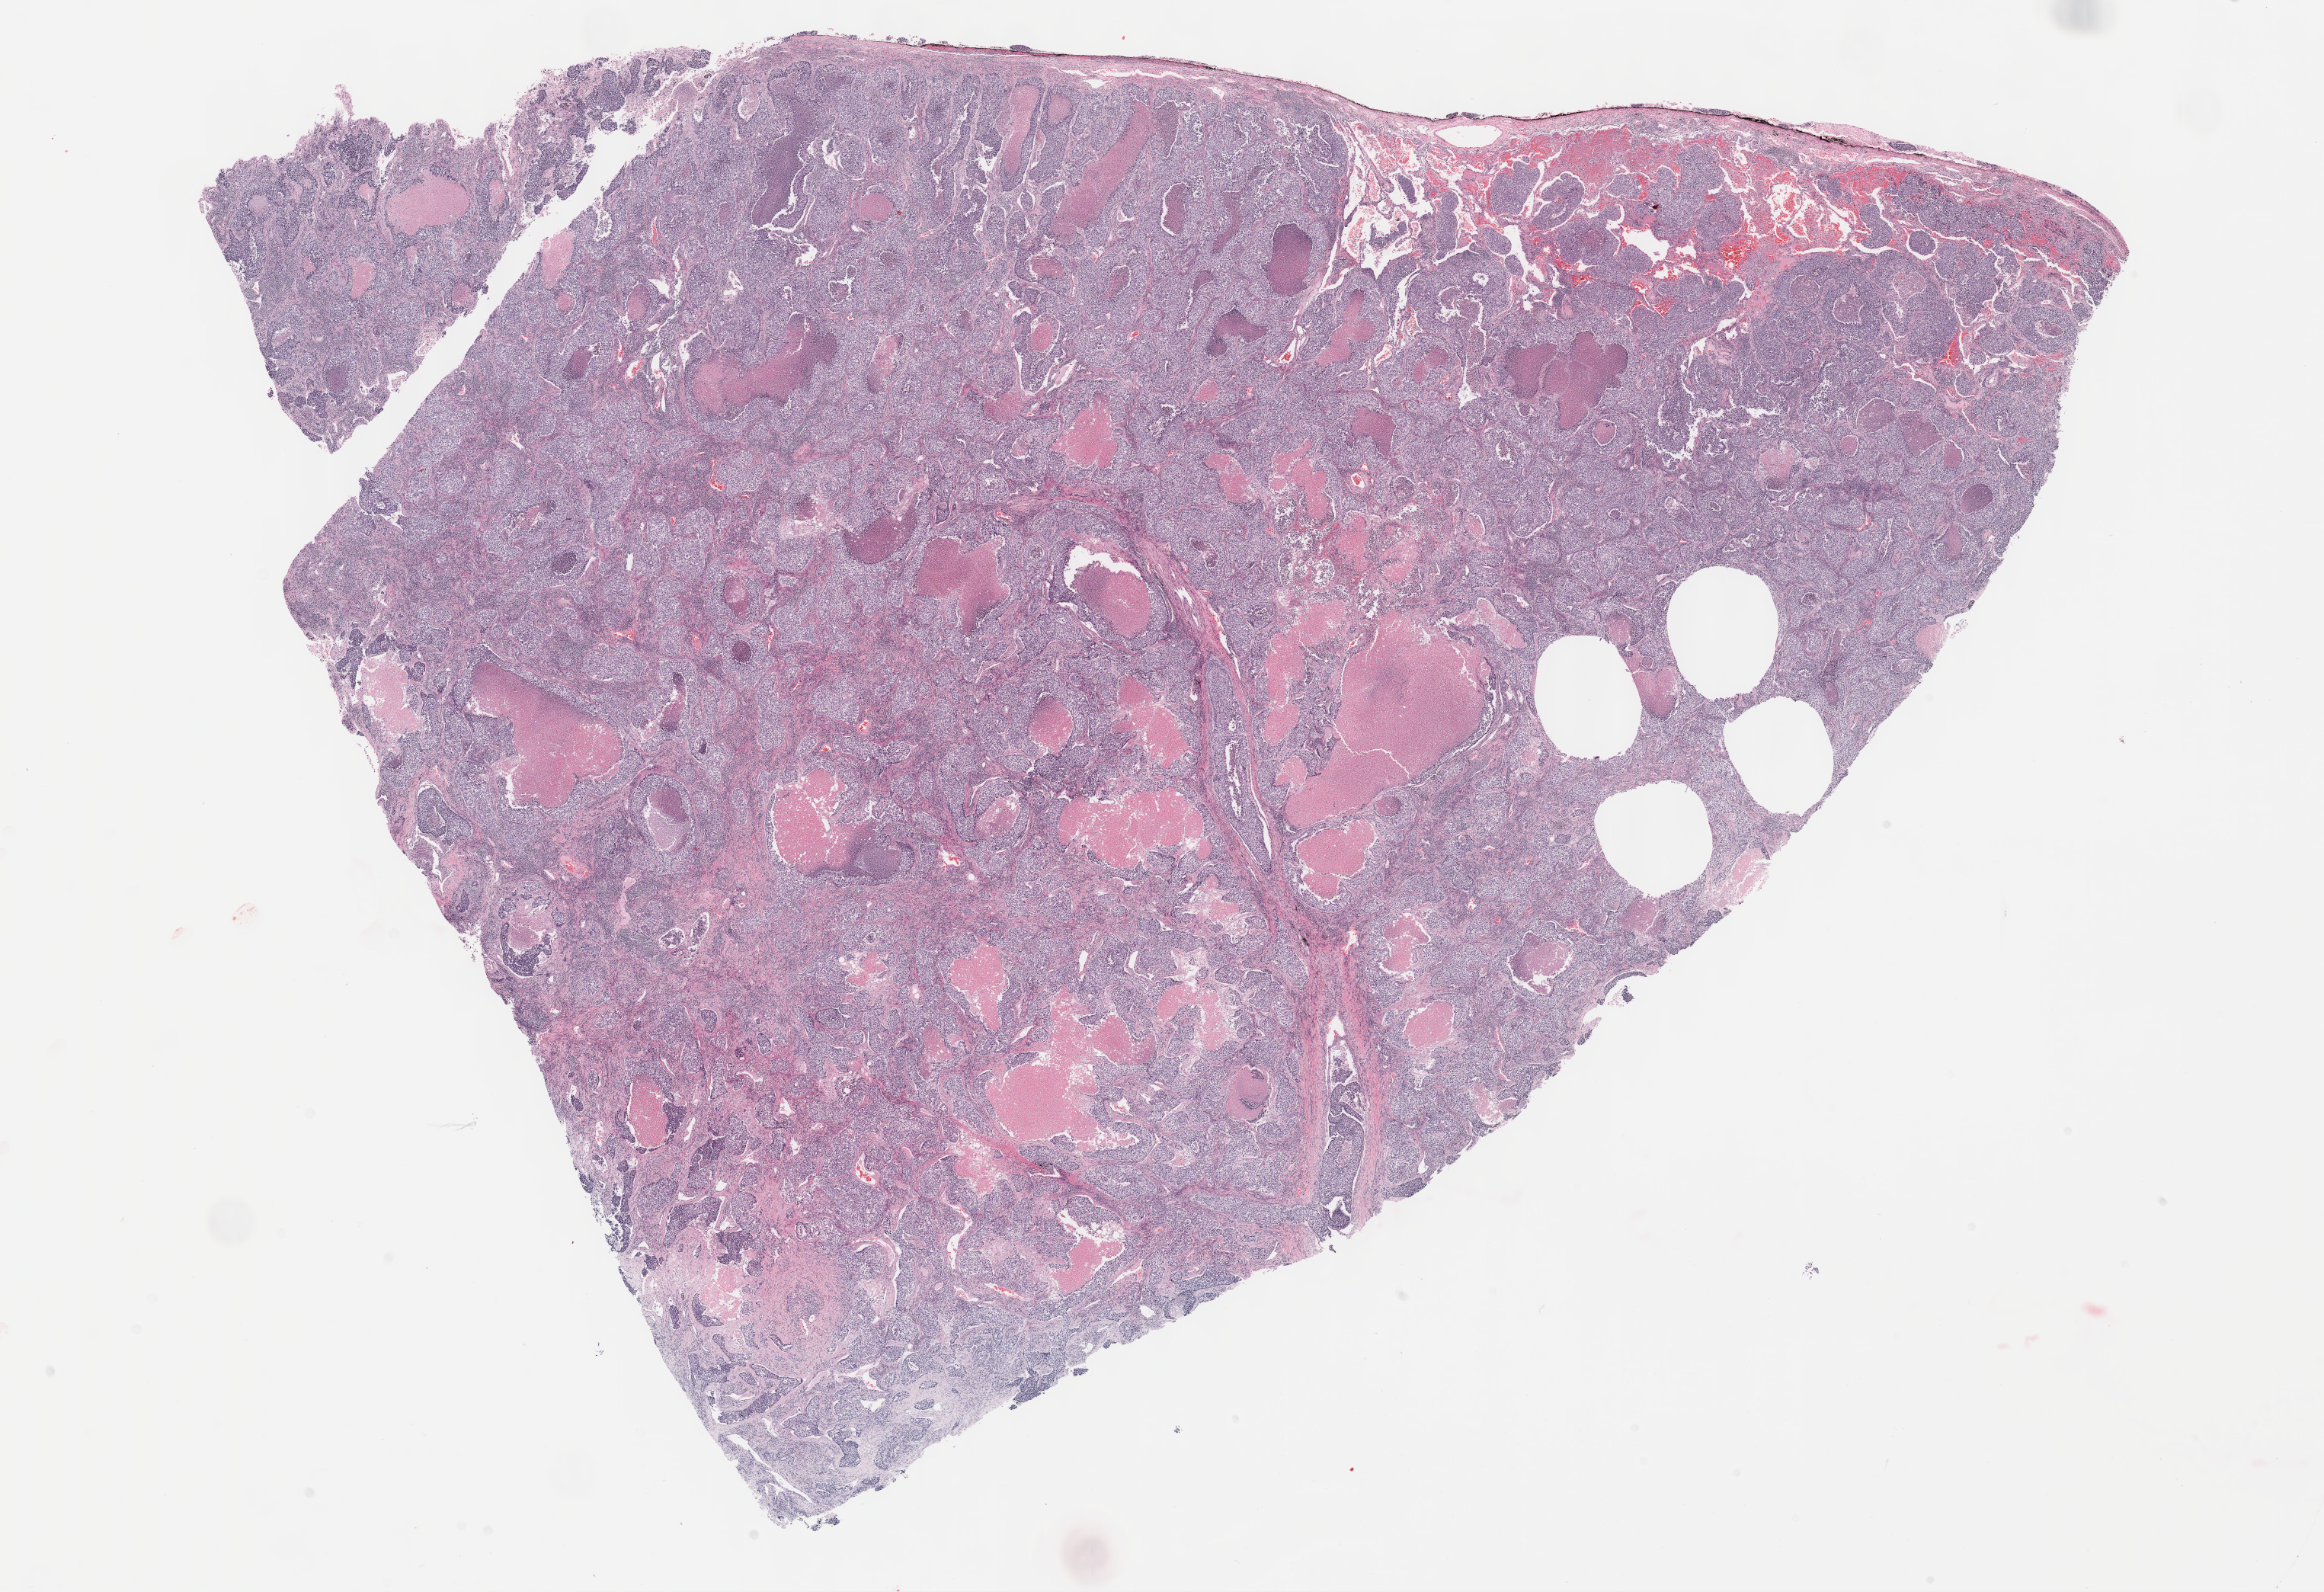
H&E-stained whole-slide image, a low-resolution overview of the entire scanned area, about 24.7 x 16.9 mm (slide scanned at 40x); formalin-fixed paraffin-embedded (FFPE) diagnostic section; primary tumour sample from the lung. Male, age 61 years at initial diagnosis.
Histologic diagnosis: Acinar cell carcinoma (lower lobe, lung). AJCC pathologic stage: IIIA (6th edition). Laterality: left.